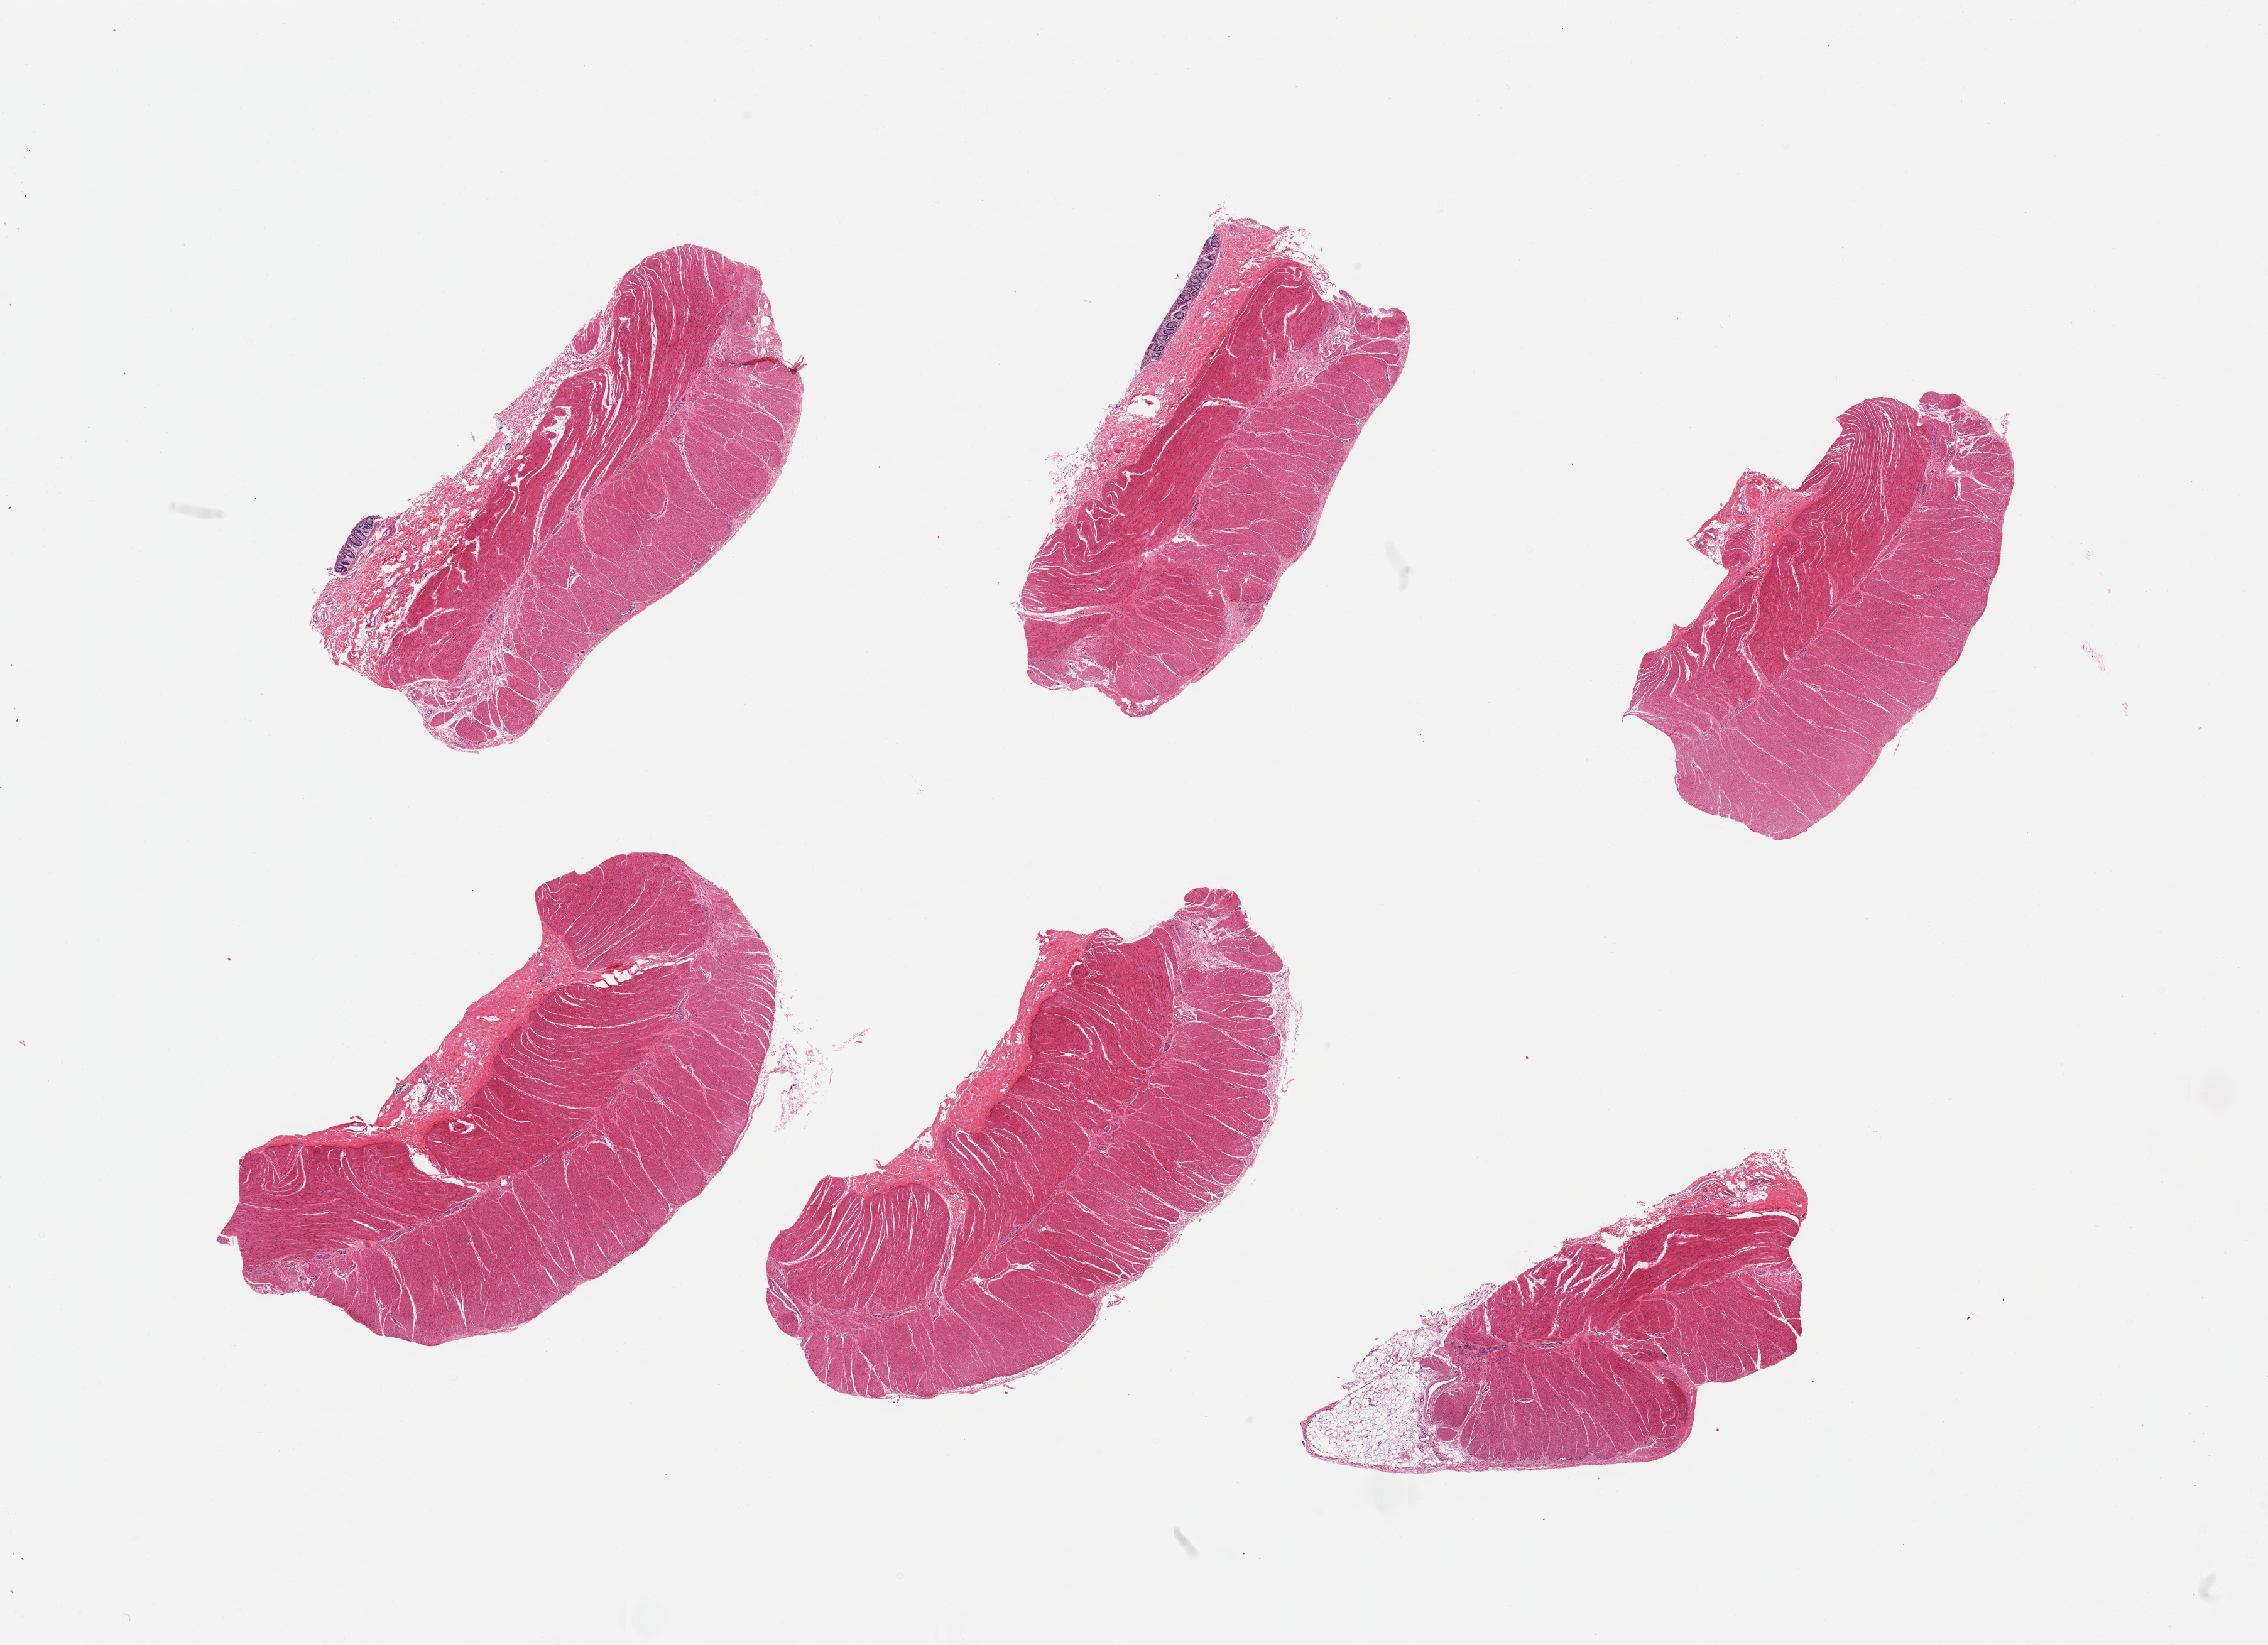
Digitized H&E-stained section, shown as a low-resolution overview of the whole scanned area (about 28.5 x 20.7 mm, acquisition: 20x scan), PAXgene-fixed paraffin-embedded (PFPE) section, sampled site (target tissue): sigmoid colon, tissue donor sample. Male donor.
Pathologist's review note for this sample: 6 pieces; target muscularis; tiny residual fragments of mucosa and attached fat.